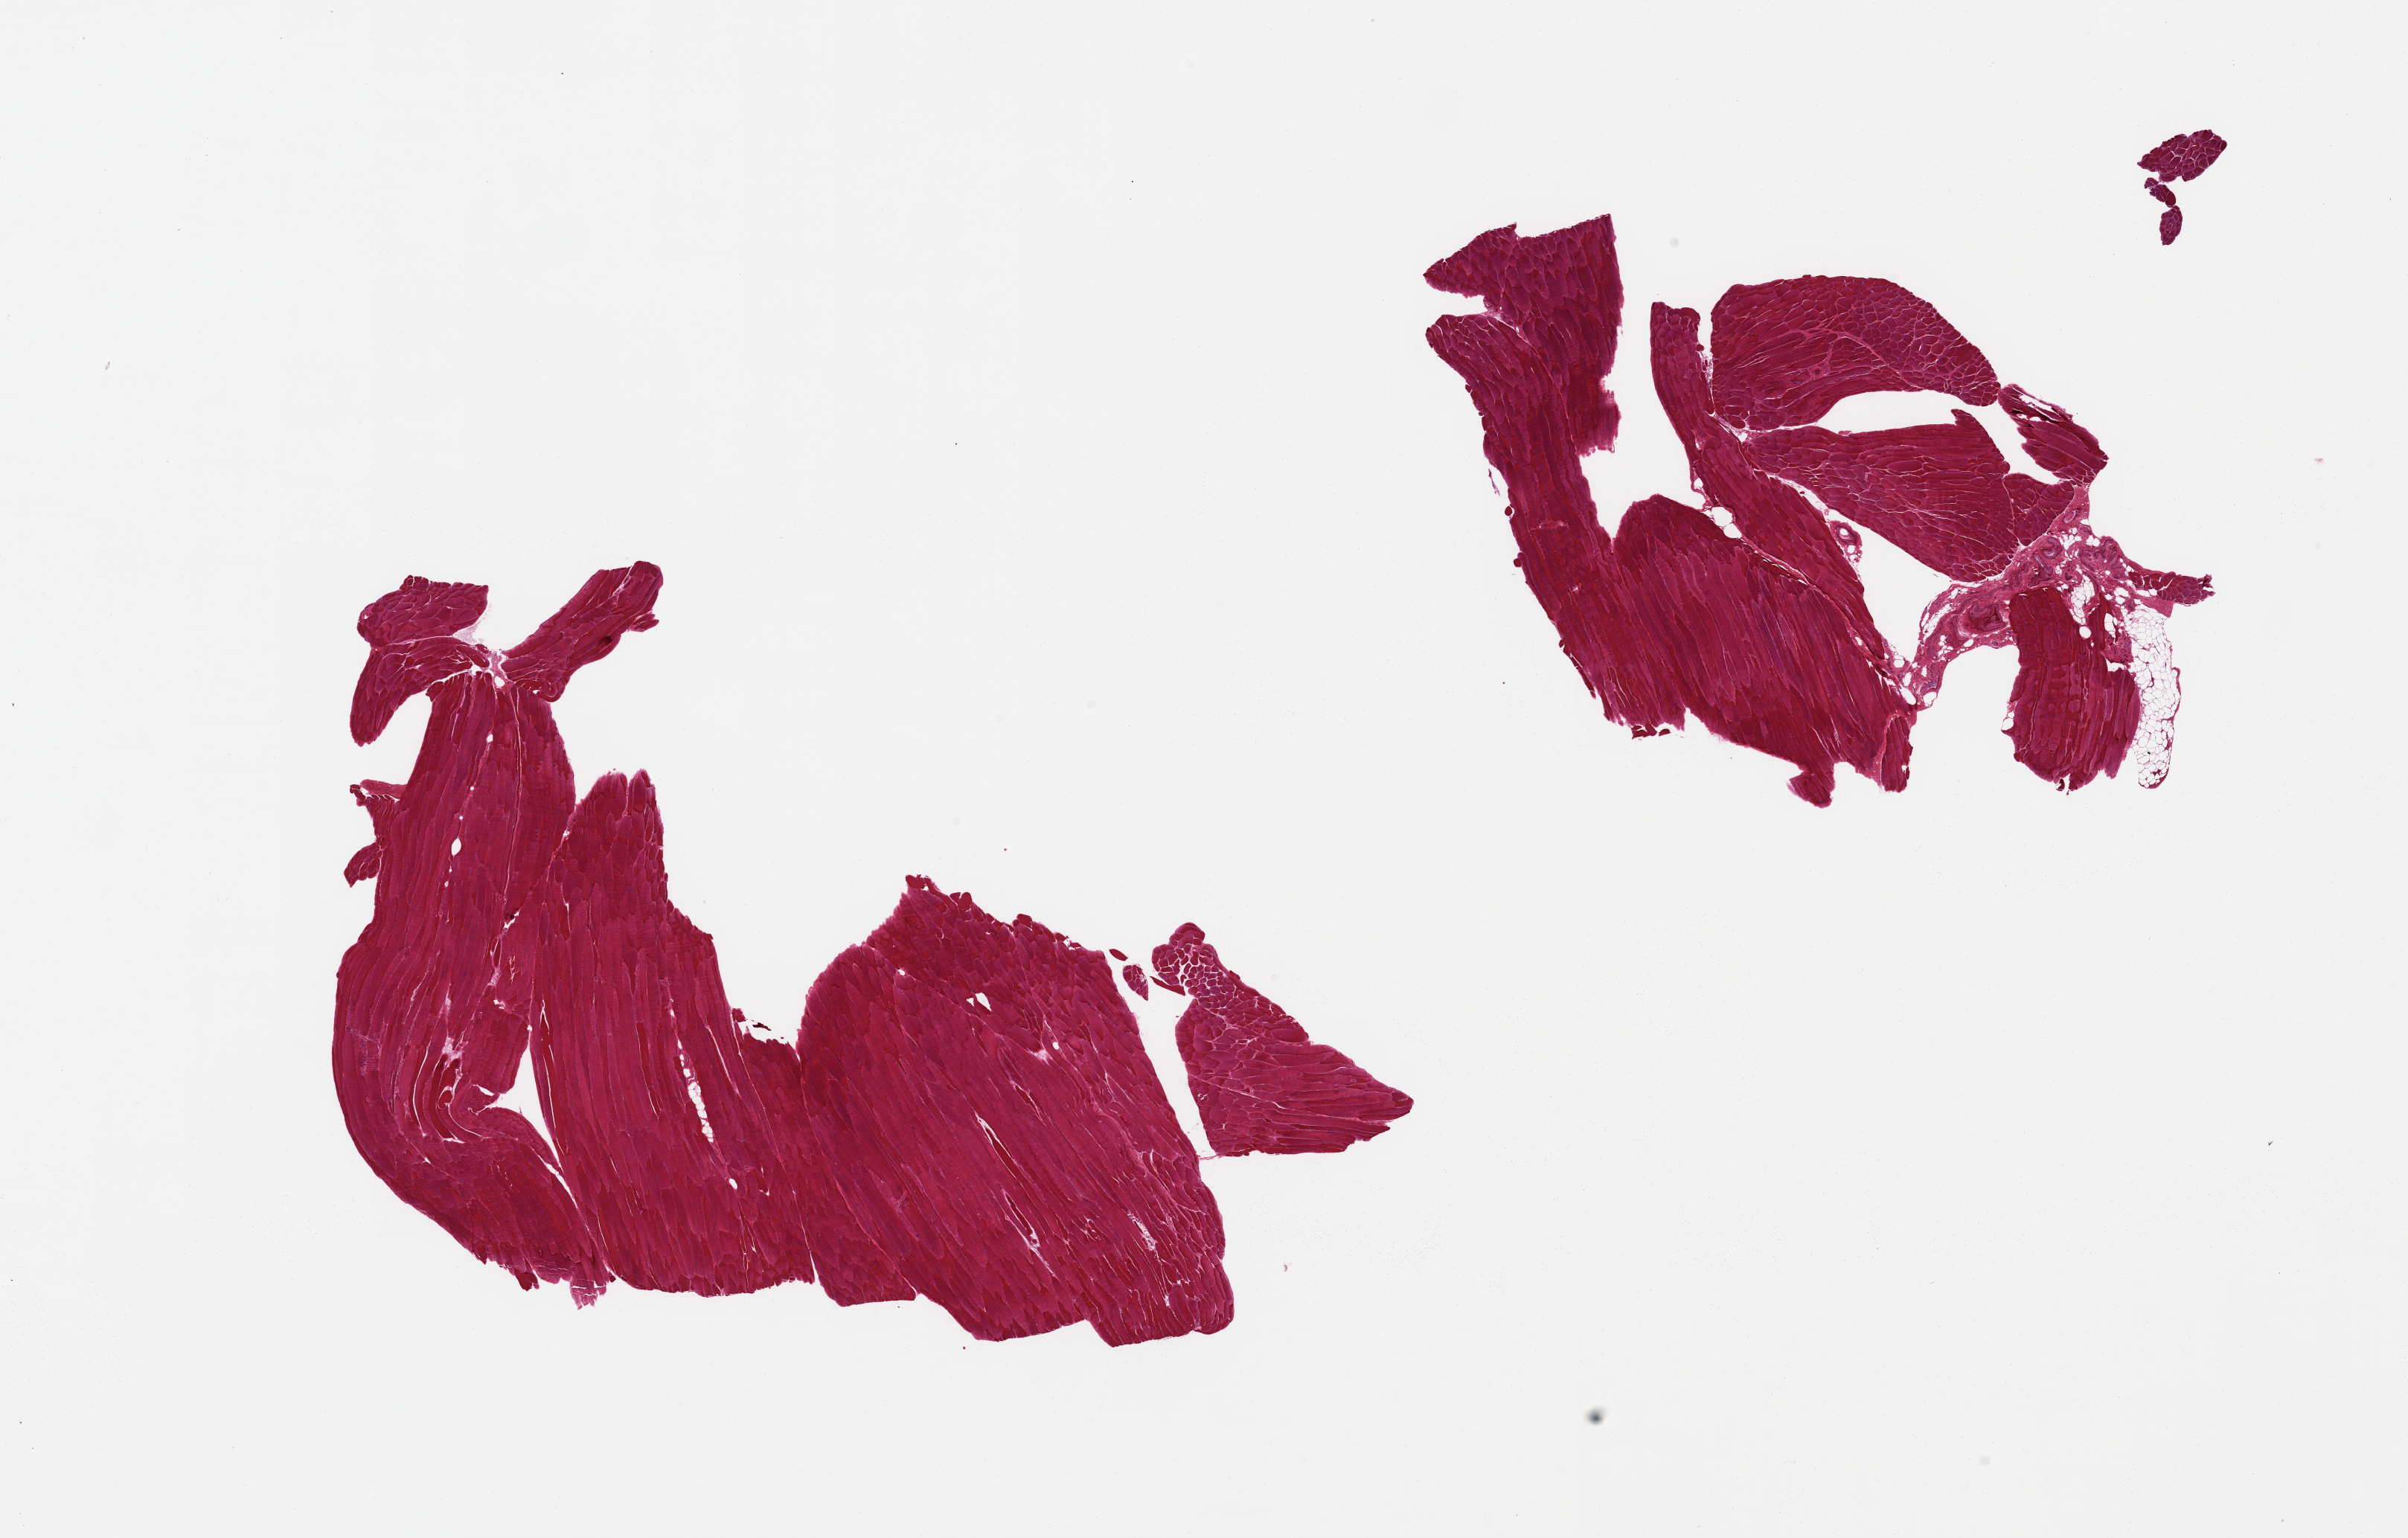
Hematoxylin and eosin (H&E) whole-slide image — whole scanned area (about 25.6 x 16.3 mm, from a 20x scan) shown as a low-resolution overview. PAXgene-fixed, paraffin-embedded tissue. Sampled site (target tissue): skeletal muscle. Donor tissue sample. Donor sex: male.
• review note (as recorded): 2 pieces, ~5-10% interstitial fat/vascular elements